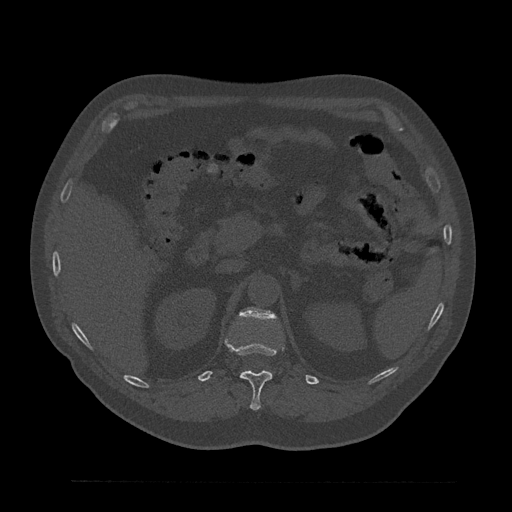
CT including the spine, one axial slice; position 210 of 797 along the scan axis; reconstruction kernel Br40s/3; bone window (W 1800 / L 400 HU); 0.5 mm slice thickness; 512 × 512 image matrix, field of view 430 × 430 mm. Patient: male, 61 years. Case-level facts recorded for this patient, not image findings: primary cancer: prostate.
Outlined on this slice (semi-automatically segmented with operator editing):
- L1 vertebra: bounding box [x1, y1, x2, y2] px = [241, 307, 275, 319]
- T12 vertebra: [225, 339, 284, 410]